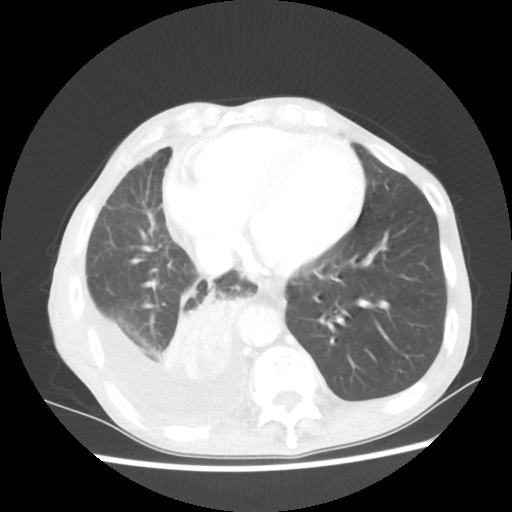
Chest CT, one axial slice; position 19 of 60 along the scan axis; 80 kVp; lung window (W 1500 / L -600 HU); 512 × 512 image matrix, field of view 335 × 335 mm. Male patient, age 76 years. Case-level facts recorded for this patient, not image findings: clinical TNM (as recorded): T3 N3 M1a; histopathological grade: G3.
Annotated regions visible in this slice (rectangle marked by the reading radiologist):
- lung tumour (recorded histology: squamous cell carcinoma): bounding box [x1, y1, x2, y2] px = [155, 290, 258, 388]